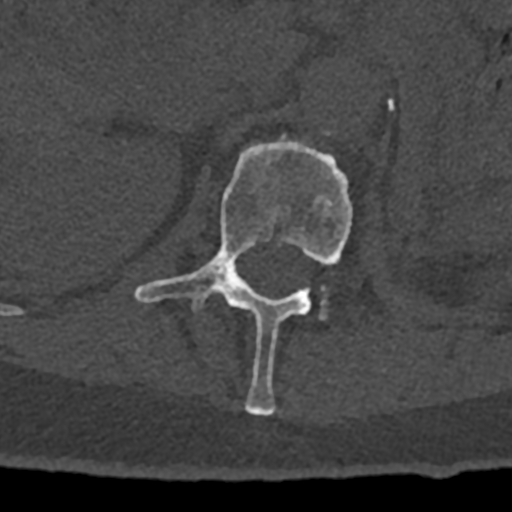
CT including the spine, one axial slice; slice 429 of 797 in the series (ordered by position); 120 kVp; bone window (W 1800 / L 400 HU); 0.5 mm slice thickness; 512 × 512 image matrix, field of view 160 × 160 mm. Patient: male, 74 years. From the clinical record (not read from this slice): primary cancer: renal.
Structures marked on this image (semi-automatic segmentation, software-assisted and operator-edited):
- L1 vertebra: box from (x=134, y=137) to (x=353, y=416) px
- L2 vertebra: (x=320, y=297)–(x=327, y=319)